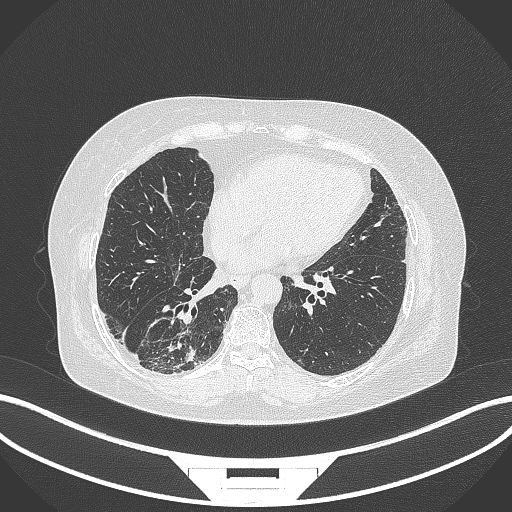
Chest CT, one axial slice. Slice 82 of 296 in the series (ordered by position). Reconstruction kernel B70f. Lung window (W 1500 / L -600 HU). 512 × 512 image matrix, field of view 400 × 400 mm. Patient: female, 65 years. From the clinical record (not read from this slice): clinical TNM (as recorded): T2b N1 M0.
Structures marked on this image (bounding box drawn by a radiologist):
- lung tumour (recorded histology: adenocarcinoma): bounding box <137,315,200,375> (left, top, right, bottom; pixels)